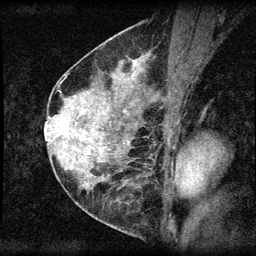
Breast MRI (dynamic contrast-enhanced), one sagittal slice. Position 26 of 60 along the scan axis. Dynamic contrast-enhanced series, image 2 of 3 at this slice position (ordered by acquisition). 1.5 T. TE 4.2 ms, TR 8.2 ms. 2 mm slice thickness. 256 × 256 image matrix, field of view 180 × 180 mm. Patient: female, 45 years.
Outlined on this slice (semi-automatic segmentation, software-assisted and operator-edited):
- analysis volume of interest (the breast-tissue region the enhancement analysis was run in; not a lesion): bounding box [x1, y1, x2, y2] px = [55, 110, 94, 148]
- tumour enhancement mask (voxels above the 70 % enhancement threshold inside the analysis volume of interest): [61, 121, 68, 132]